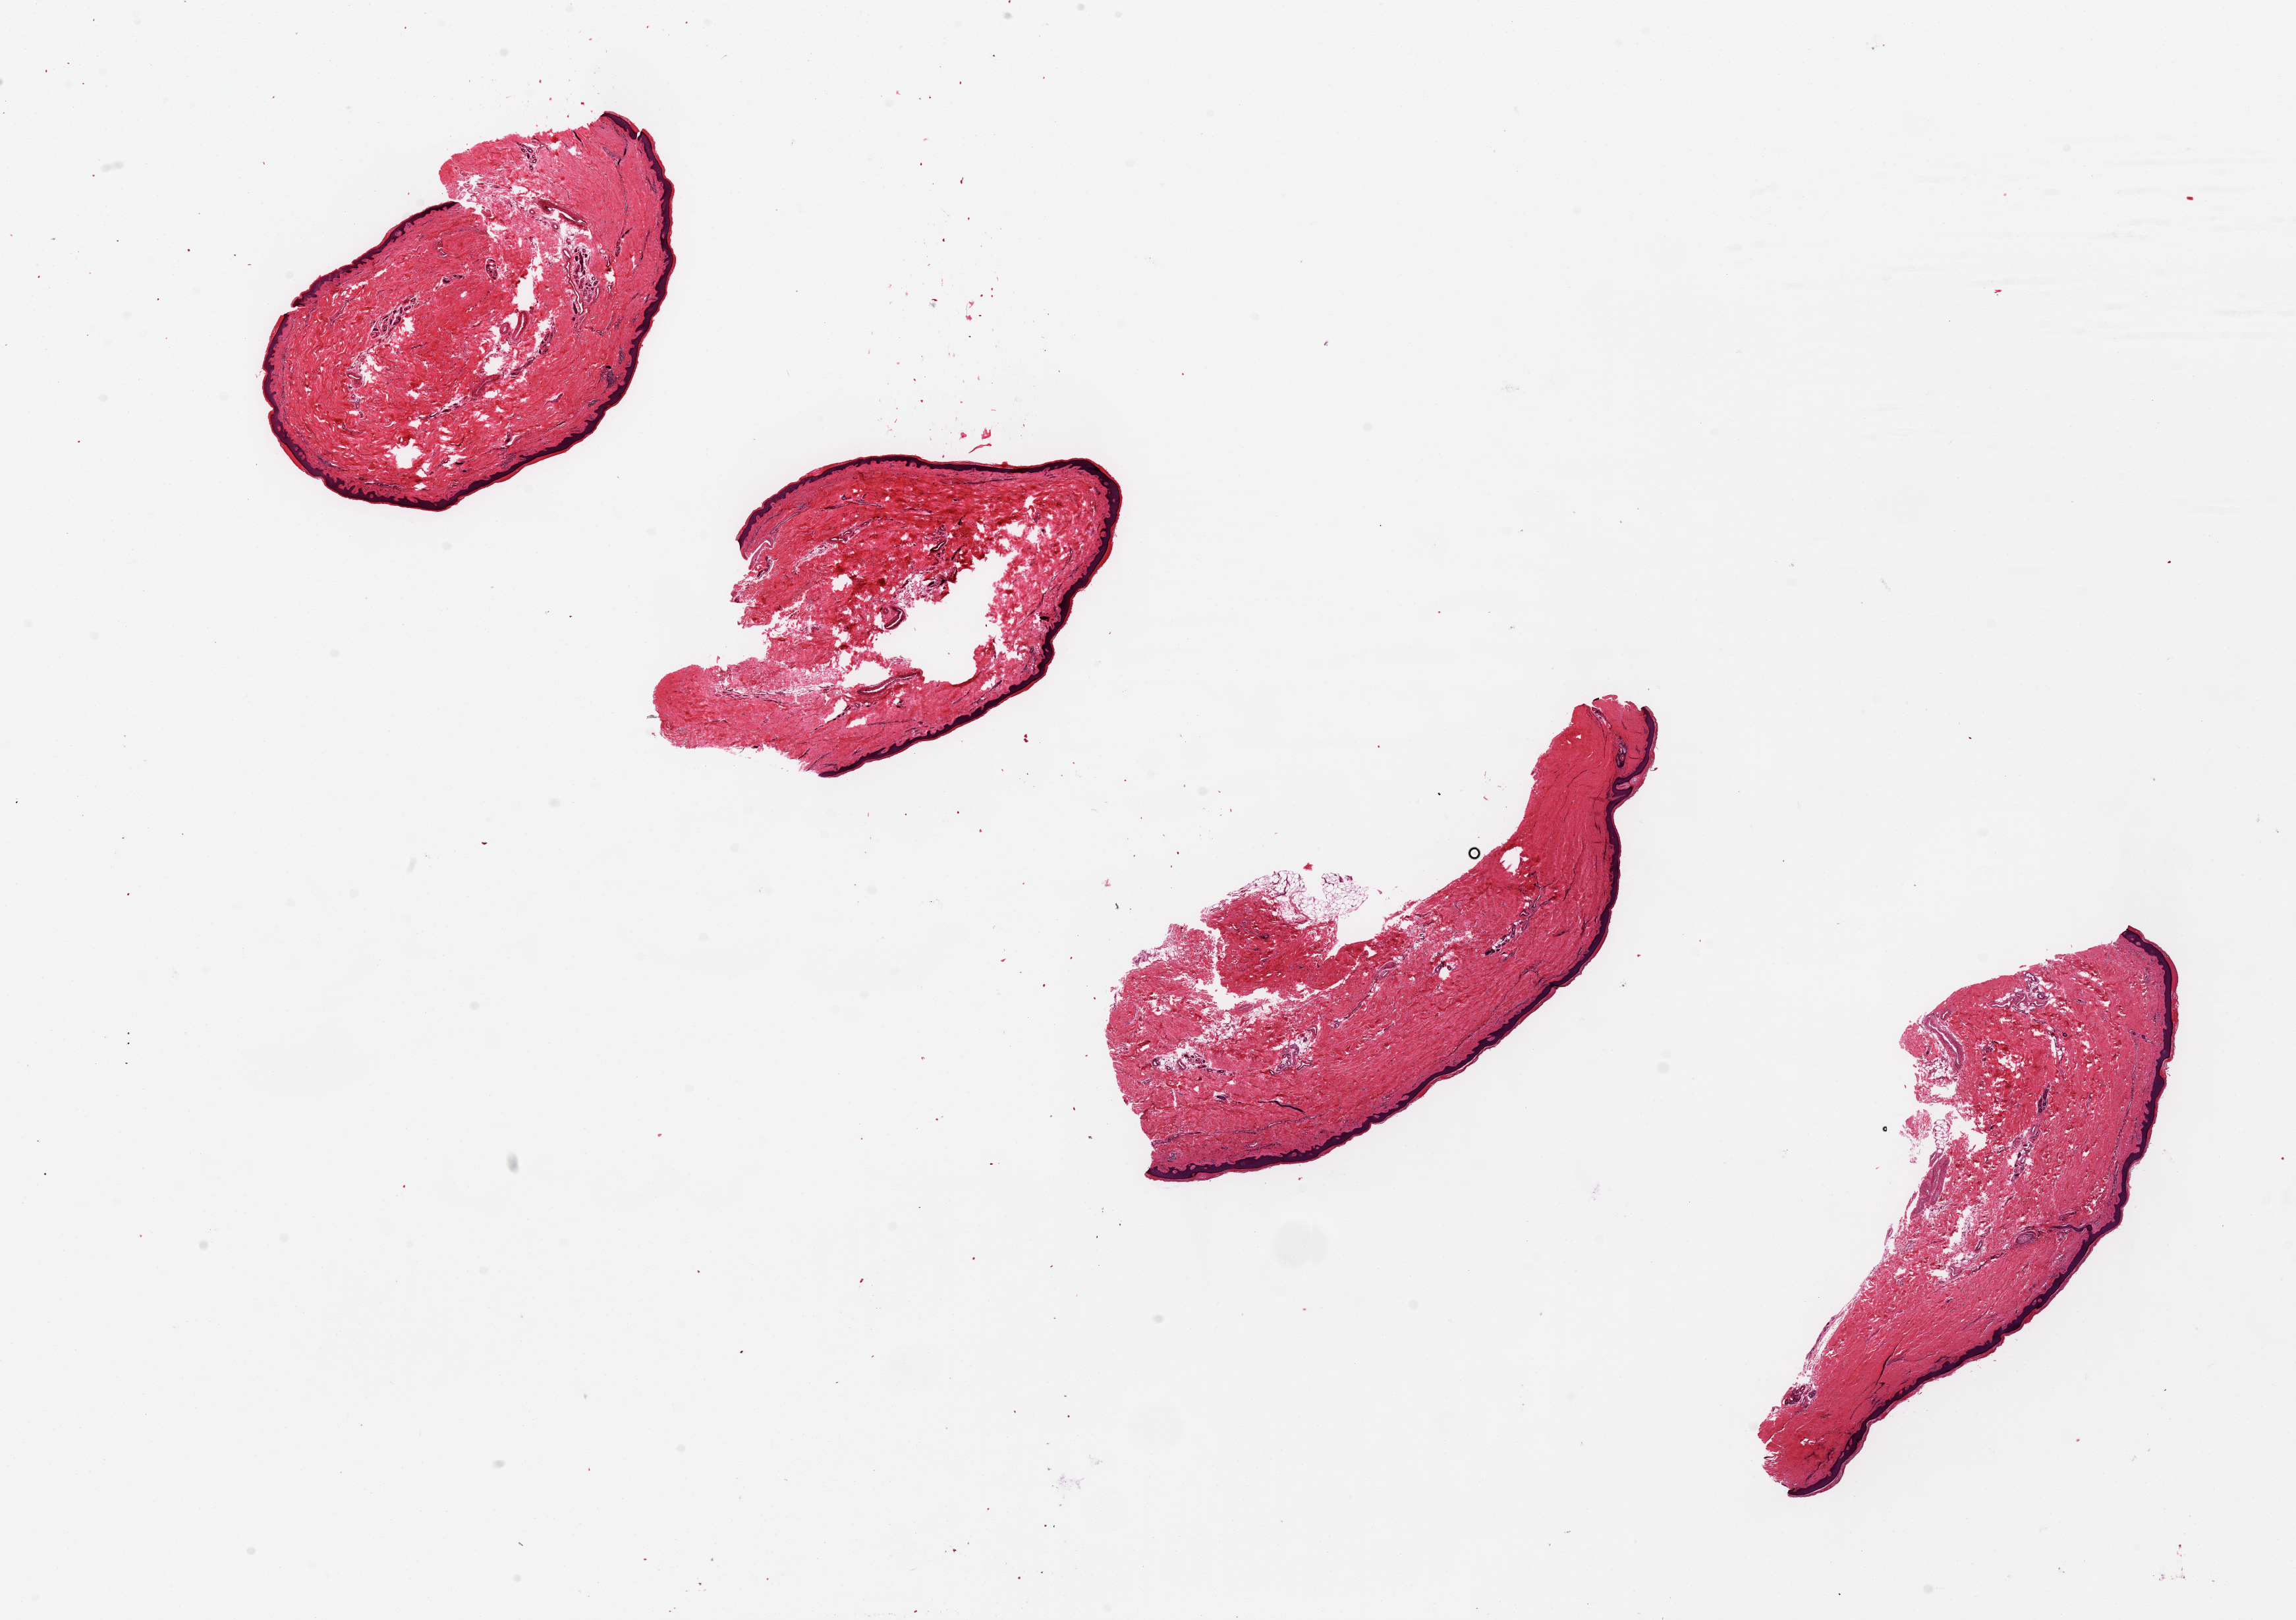
Whole-slide image, hematoxylin and eosin (H&E) stain, a low-resolution overview of the entire scanned area, about 27.6 x 19.4 mm (acquisition: 20x scan); PAXgene-fixed paraffin-embedded (PFPE) section; target tissue: skin of lower leg; tissue donor sample. Donor: male.
• reviewer comment on this tissue sample: Epidermis is 3-5% of specimen thickness